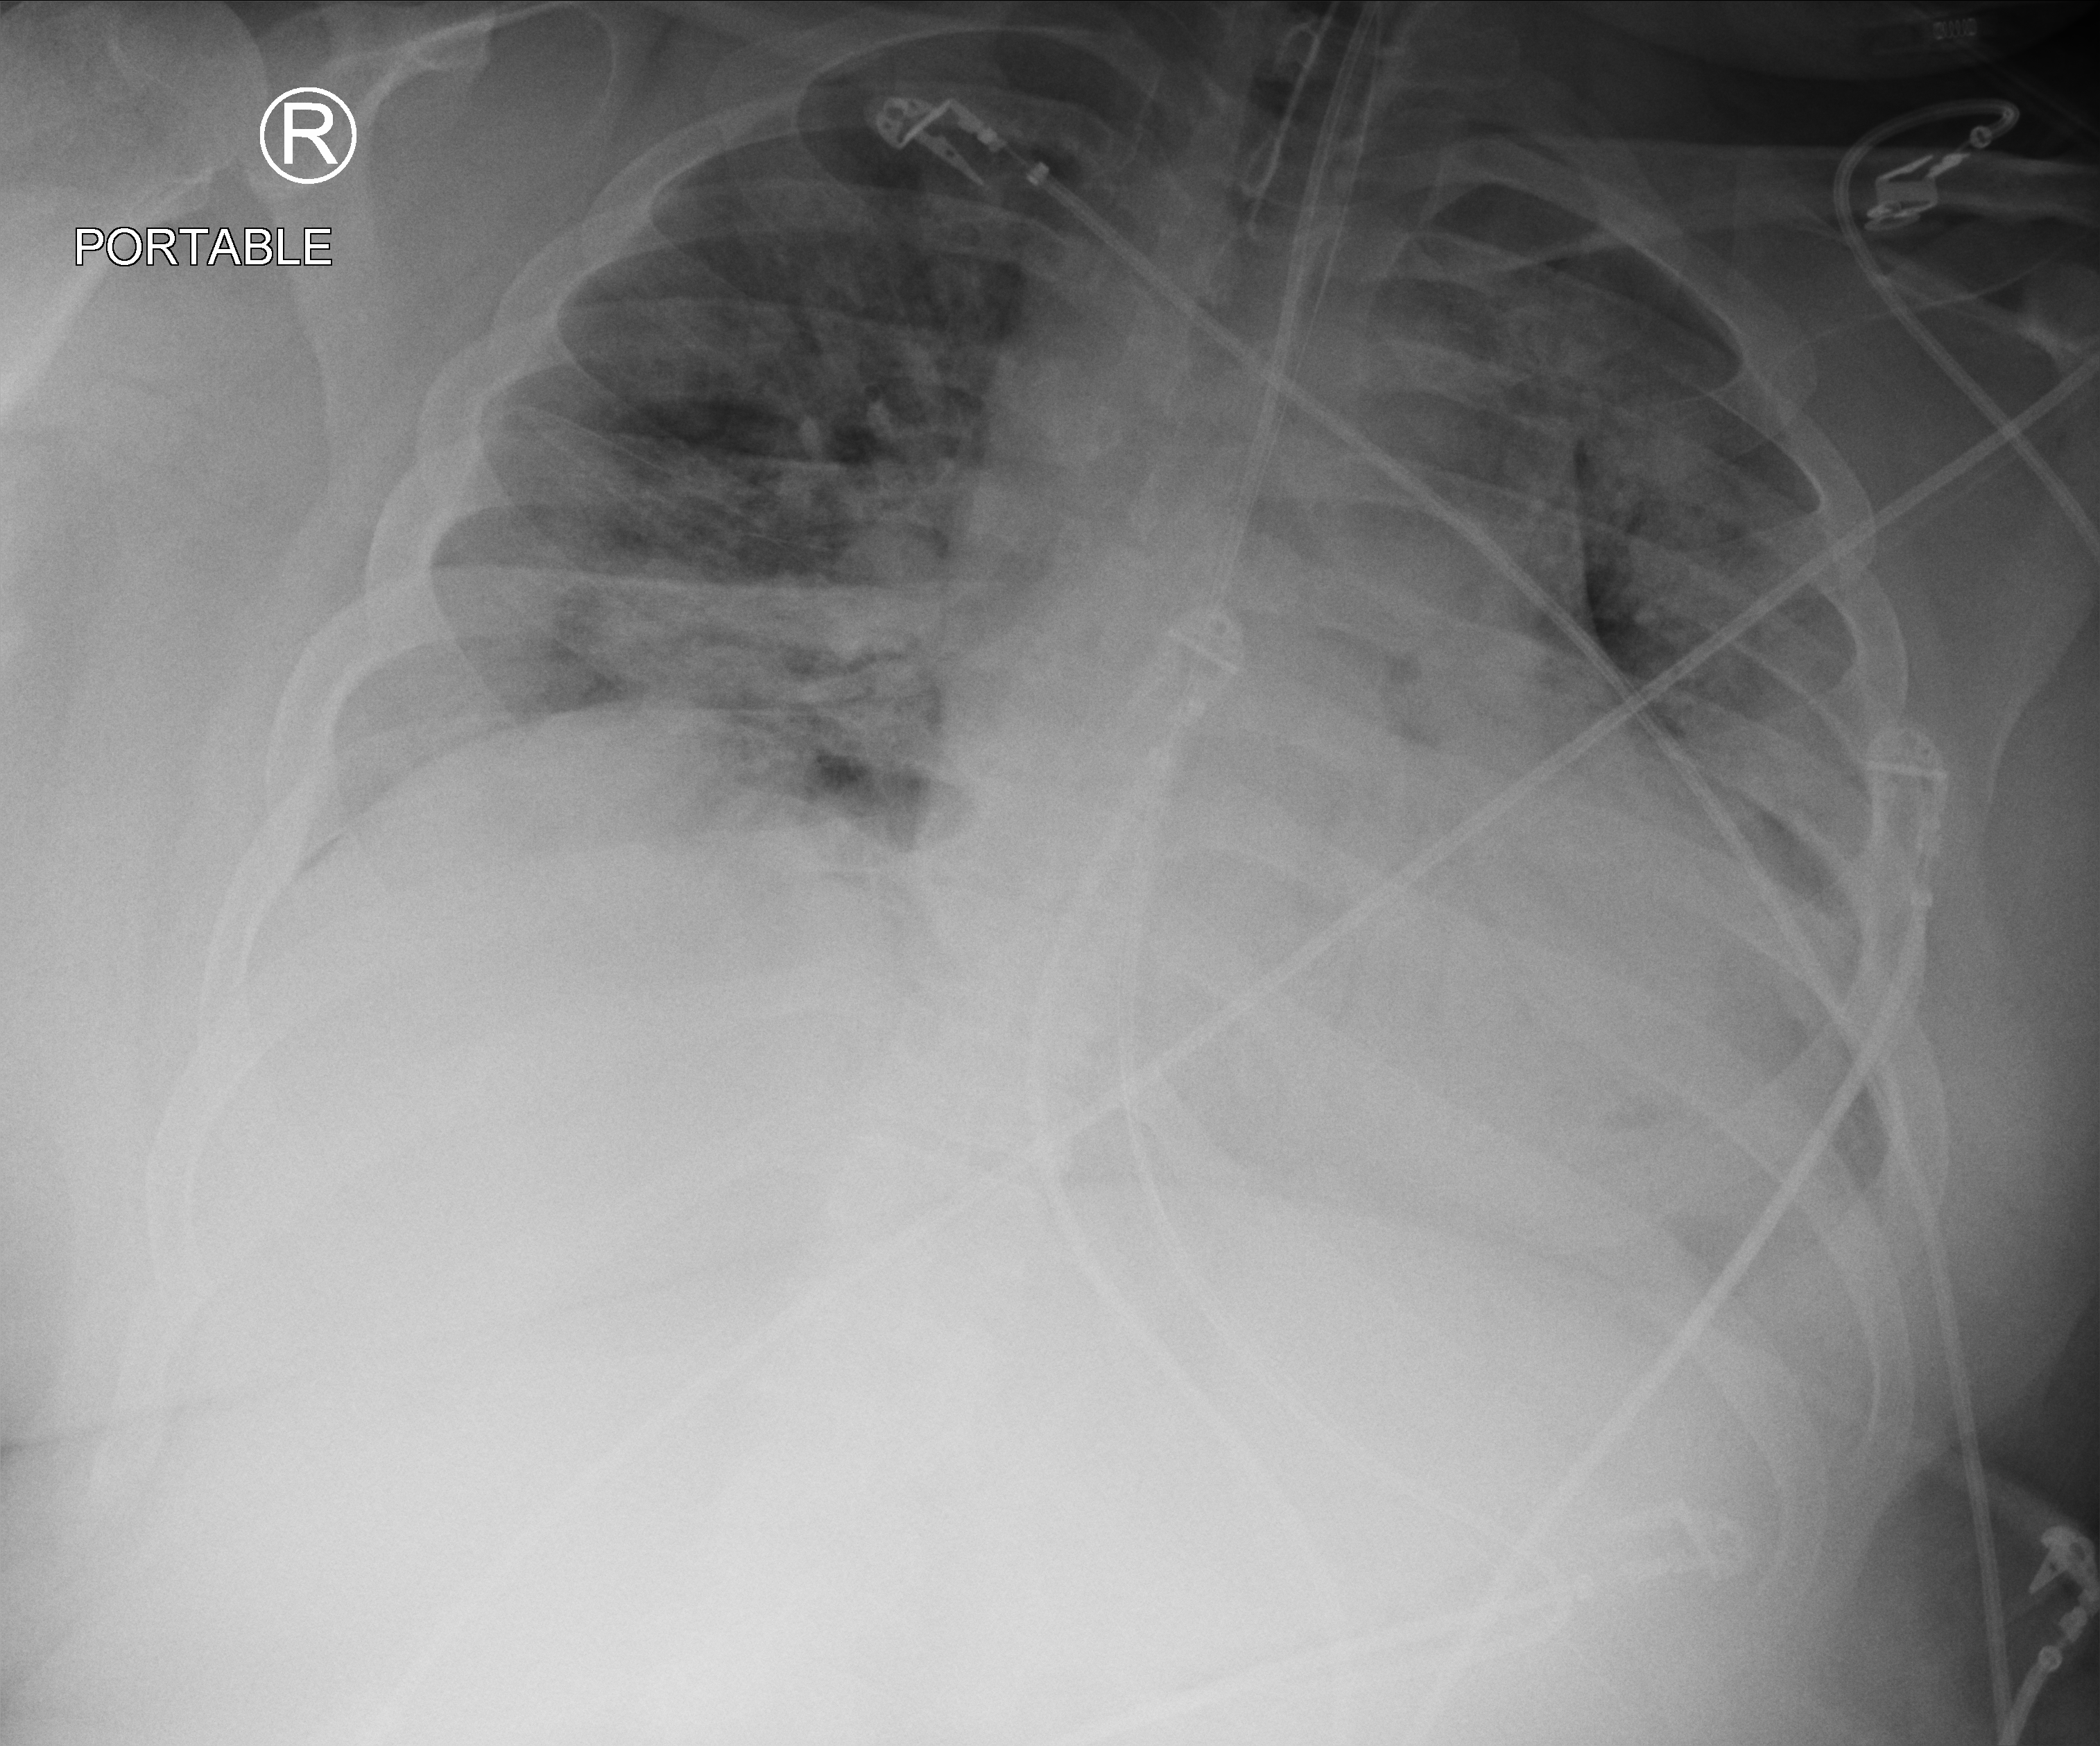
Chest X-ray (portable); anteroposterior (AP) projection. Adult patient hospitalised with COVID-19, age 18–59 years.
From the hospital-stay record, not from the radiograph (when in the stay this image was taken is not recorded): length of hospital stay: 10 days; admitted to intensive care during this hospital stay: yes; mechanically ventilated during this hospital stay: yes.